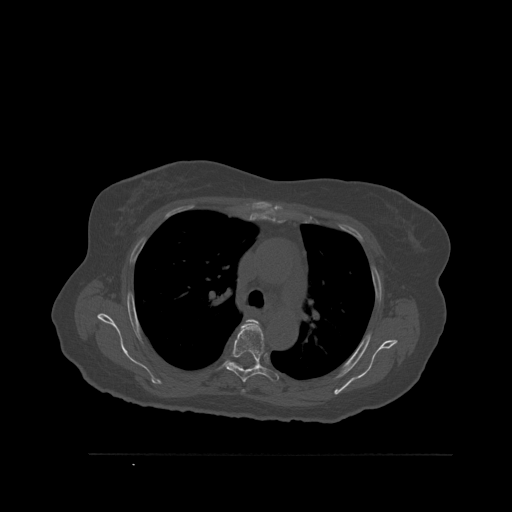
CT including the spine, one axial slice; position 395 of 527 along the scan axis; bone window (W 1800 / L 400 HU); 512 × 512 image matrix, field of view 470 × 470 mm. Patient: female, 73 years. Case-level facts recorded for this patient, not image findings: primary cancer: breast; vertebrae with lytic lesions (as recorded): L2.
Annotated regions visible in this slice (semi-automatically segmented with operator editing):
- T4 vertebra: bounding box <242,319,261,393> (left, top, right, bottom; pixels)
- T5 vertebra: <225,324,278,383>